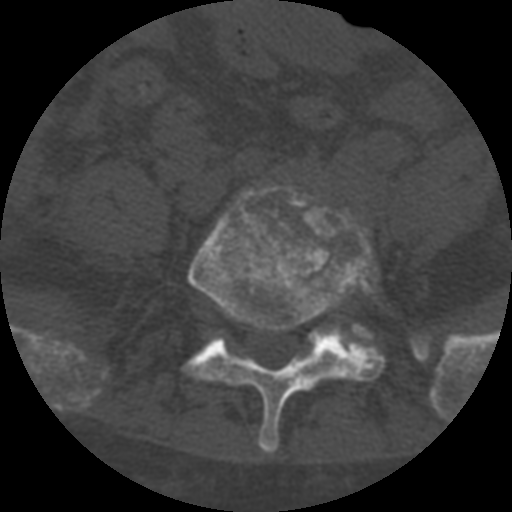
CT including the spine, one axial slice. Slice 182 of 708 in the series (ordered by position). 120 kVp. One of 3 acquisitions stored at this slice position. Bone window (W 1800 / L 400 HU). 512 × 512 image matrix, field of view 160 × 160 mm. Patient age 55 years. Case-level facts recorded for this patient, not image findings: primary cancer: colon; vertebrae with lytic lesions (as recorded): T12, L1, L5.
Outlined on this slice (semi-automatic segmentation, software-assisted and operator-edited):
- L5 vertebra: bounding box <186,184,386,454> (left, top, right, bottom; pixels)